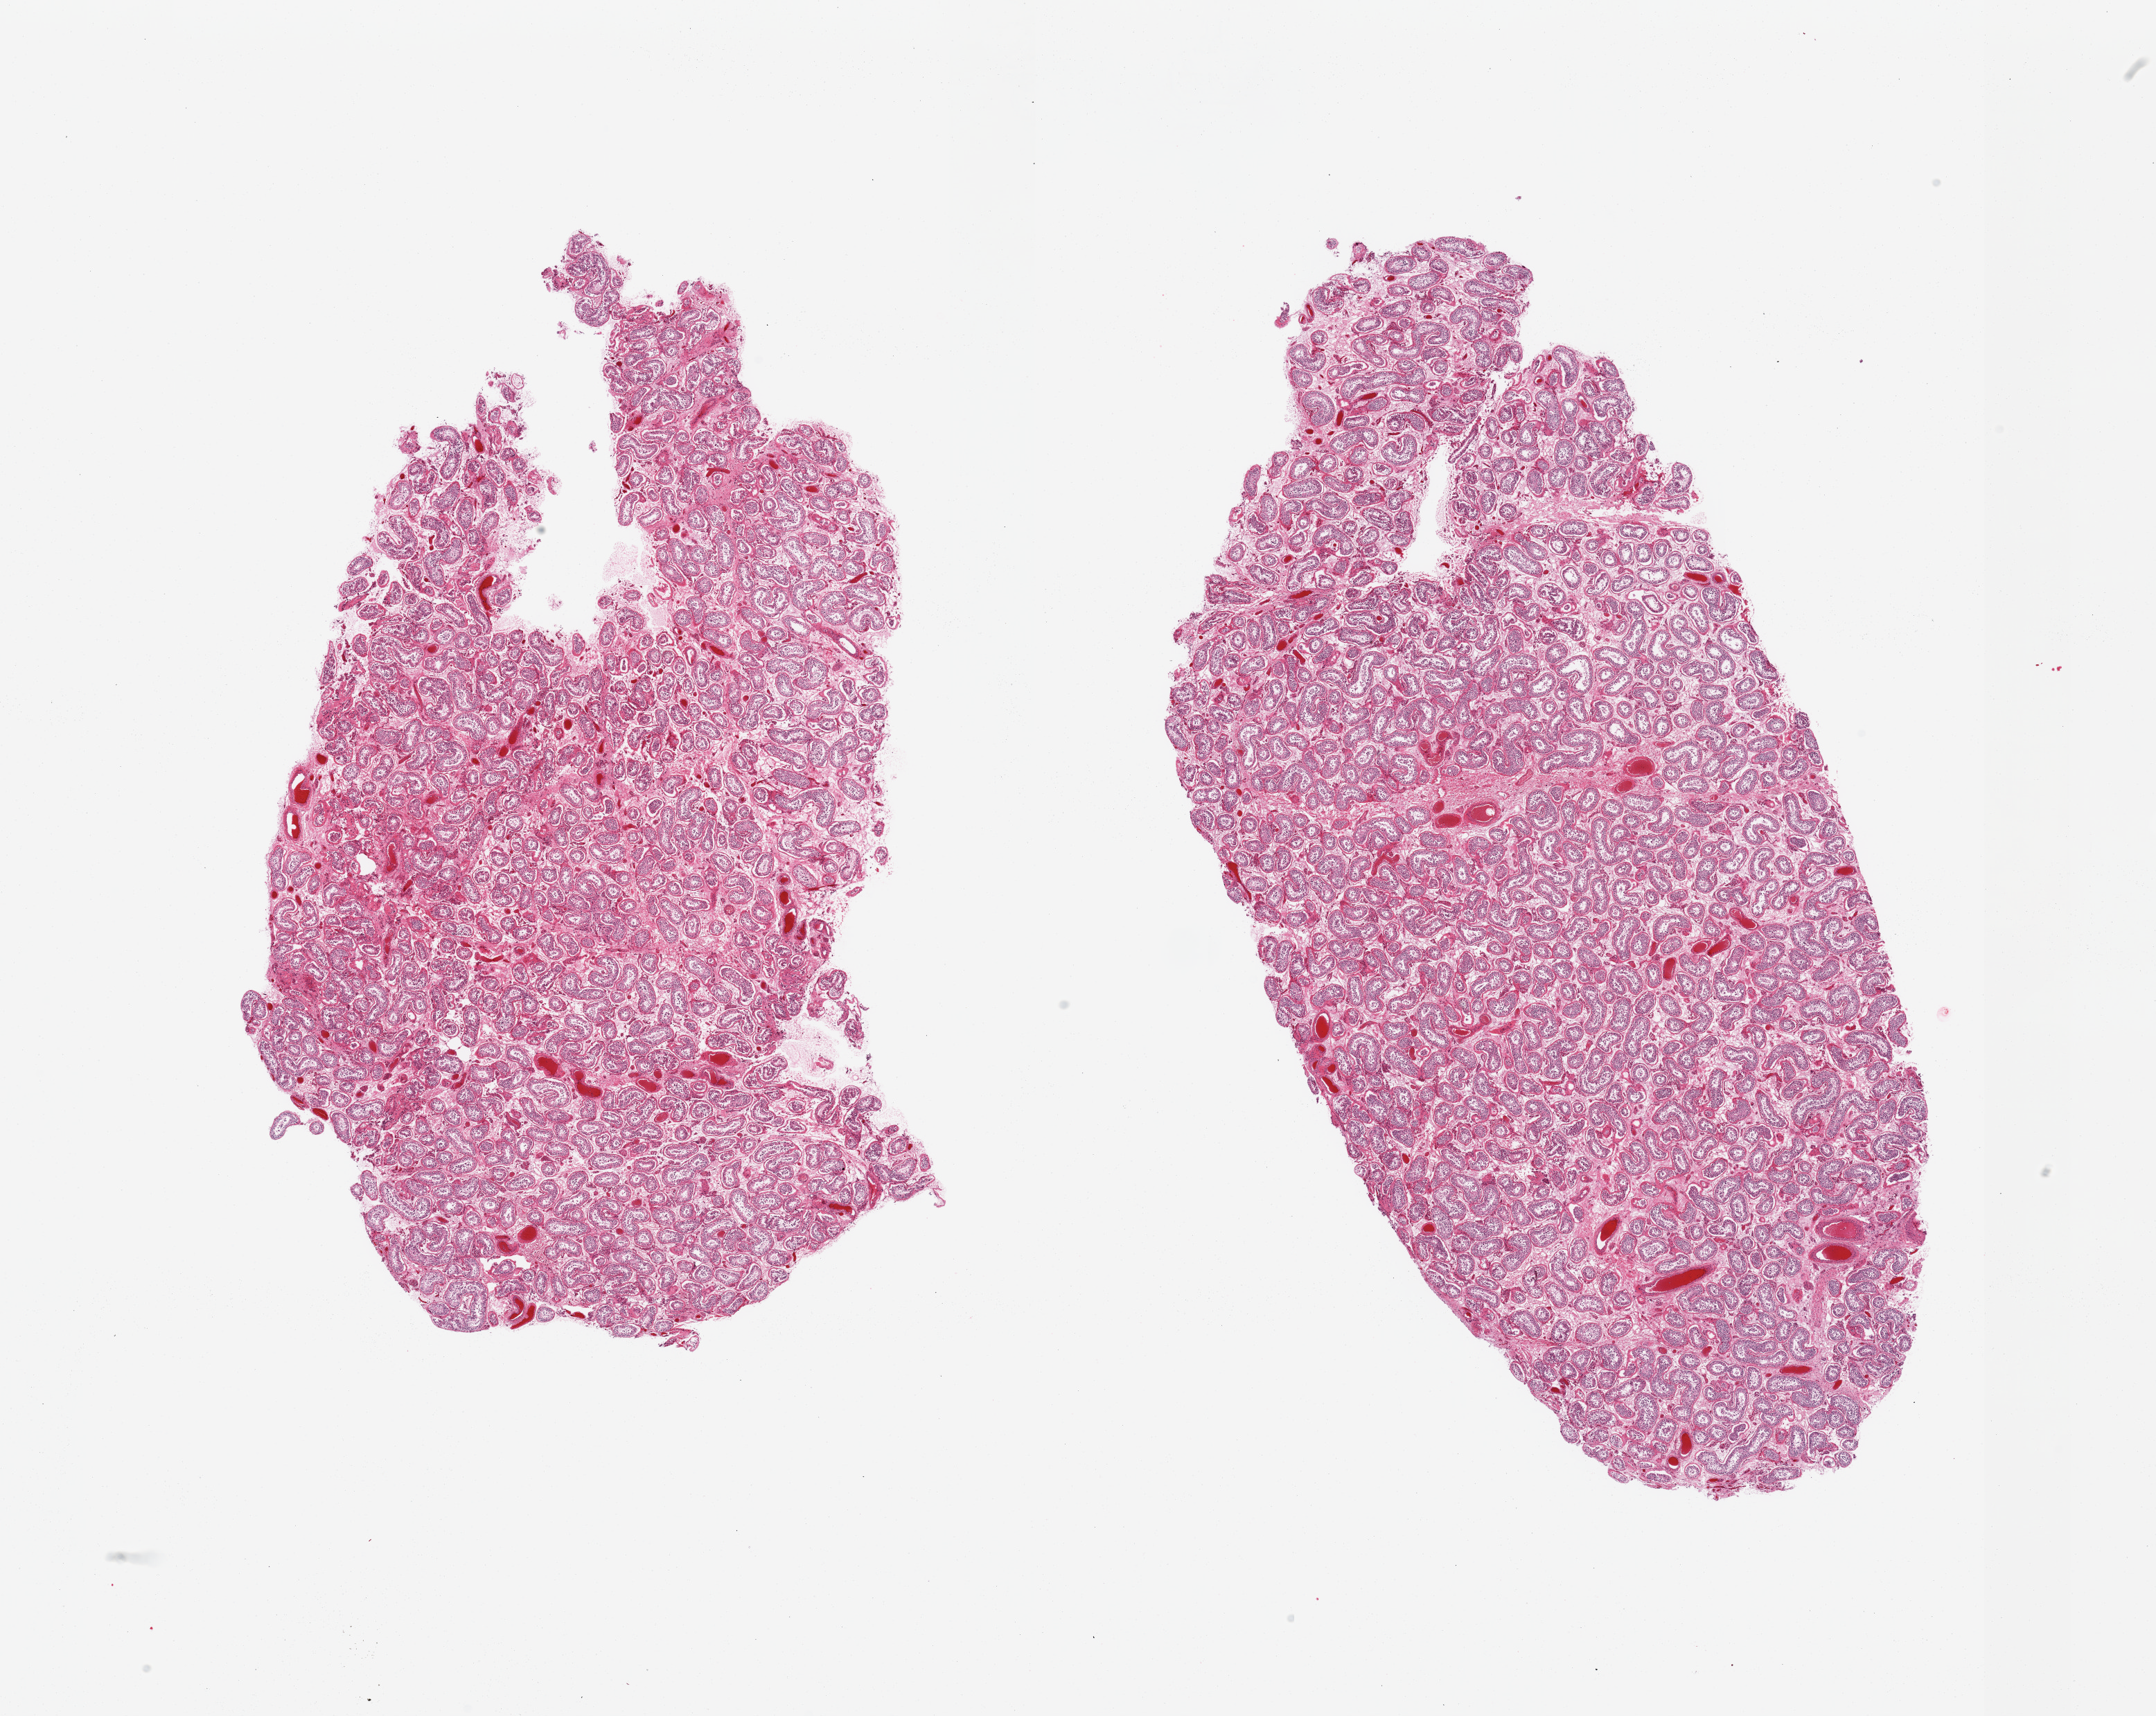
Whole-slide image, H&E stain, a low-resolution overview of the entire scanned area, about 24.6 x 19.6 mm, PAXgene-fixed paraffin-embedded (PFPE) section, target tissue: testis, tissue donor sample. Donor sex: male.
Pathologist's review note for this sample: 2 pieces; spermatogenesis present; congestion.